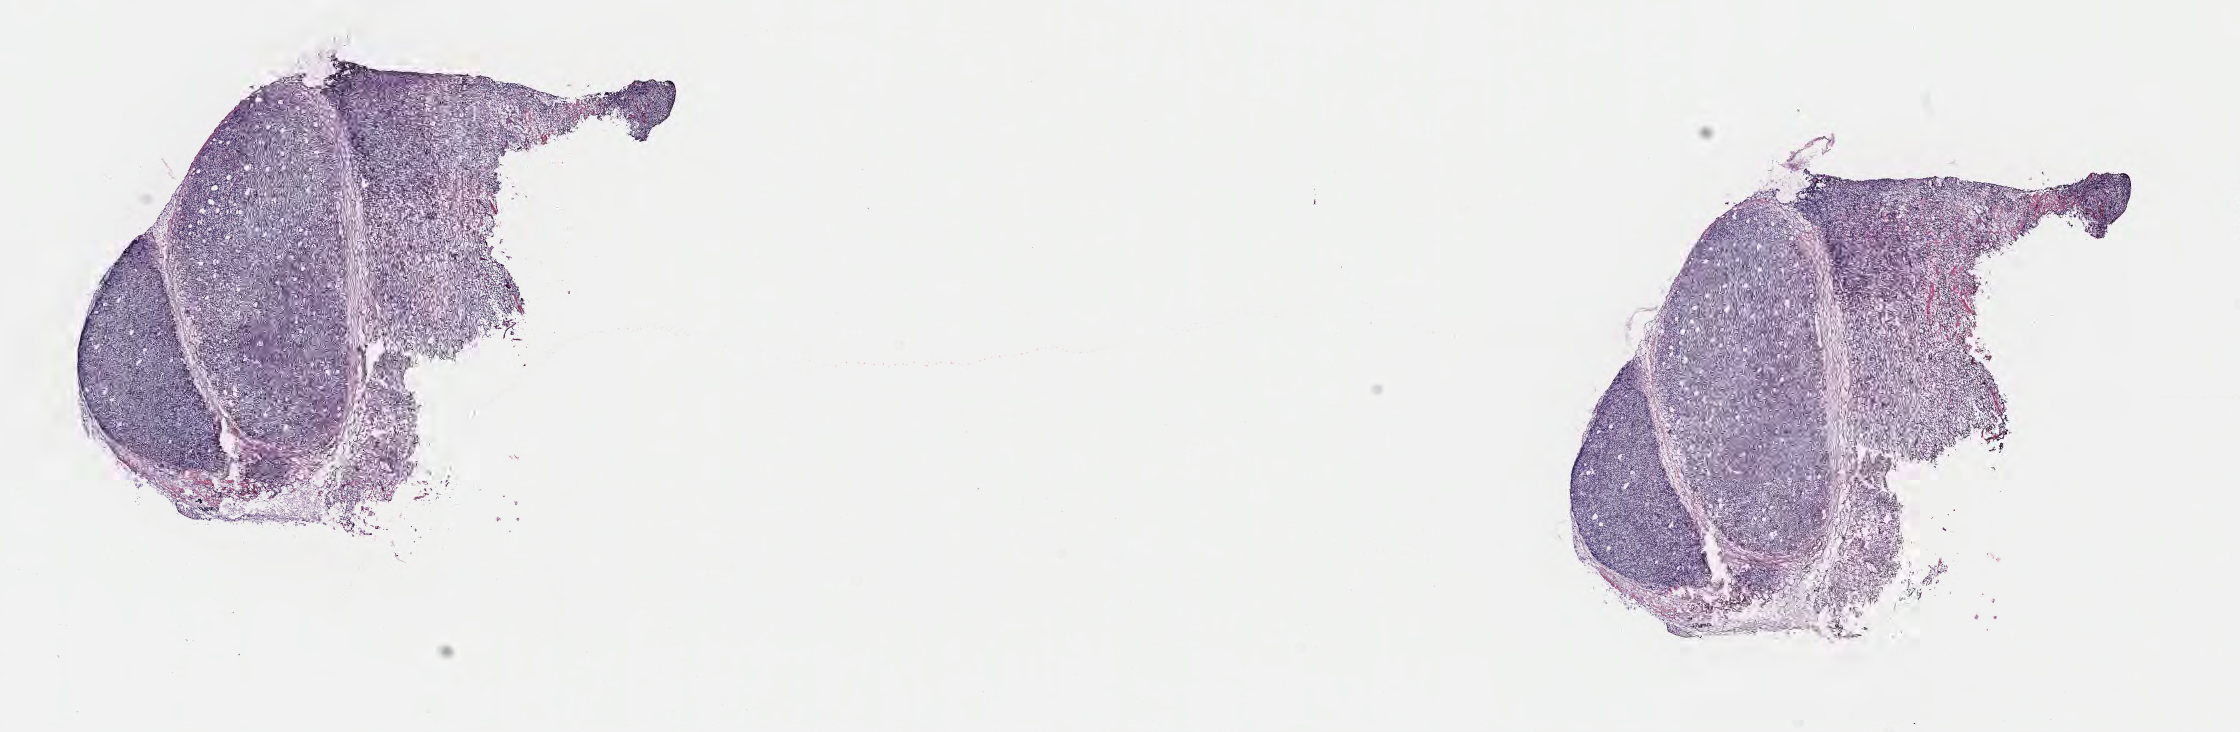
Hematoxylin and eosin (H&E) whole-slide image, low-resolution overview of the scanned area, about 18.1 x 5.9 mm, frozen section, specimen: primary tumor, anatomic site: lymph node of head and neck. Patient male; 25 years old. Composition of this section per pathologist review: tumor cells 90%, tumor nuclei 95%, stromal cells 5%, necrosis 5%, normal cells 0%. Inflammatory infiltration, as recorded: lymphocyte infiltration 40%, monocyte infiltration 30%, neutrophil infiltration 0%.
• diagnosis: Malignant lymphoma, non-Hodgkin, NOS